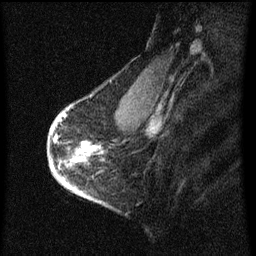
Breast MRI (dynamic contrast-enhanced), one sagittal slice. Slice 47 of 60 in the series (ordered by position). Dynamic contrast-enhanced series, image 2 of 3 at this slice position (ordered by acquisition). 1.5 T. TE 4.2 ms, TR 8 ms. 256 × 256 image matrix, field of view 180 × 180 mm. Female patient, age 56 years.
Structures marked on this image (semi-automatic segmentation, software-assisted and operator-edited):
- analysis volume of interest (the breast-tissue region the enhancement analysis was run in; not a lesion): box from (x=50, y=110) to (x=99, y=193) px
- tumour enhancement mask (voxels above the 70 % enhancement threshold inside the analysis volume of interest): (x=58, y=114)–(x=97, y=191)